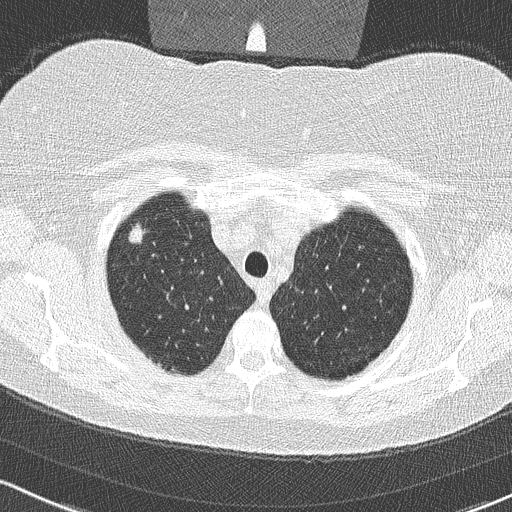
Chest CT (low-dose screening protocol), one axial image. Third screening round (two years after baseline). Lung window (W 1500 / L -600 HU). 2 mm slice thickness. 512 × 512 image matrix, field of view 320 × 320 mm. Female, age 58 years at enrolment. Former smoker at enrolment.
Expert-annotated lung lesion, bounding box (x1, y1, x2, y2) in pixels: (120, 218, 160, 255). The screening reader recorded 2 non-calcified nodules or masses ≥4 mm on this exam (right upper lobe, right lower lobe); which of them this box marks is not recorded. Later outcome: lung cancer diagnosed 48 days after this screen — bronchiolo-alveolar adenocarcinoma, NOS, right upper lobe, well differentiated (G1), stage IA (AJCC 6th edition), 9 mm at pathology.